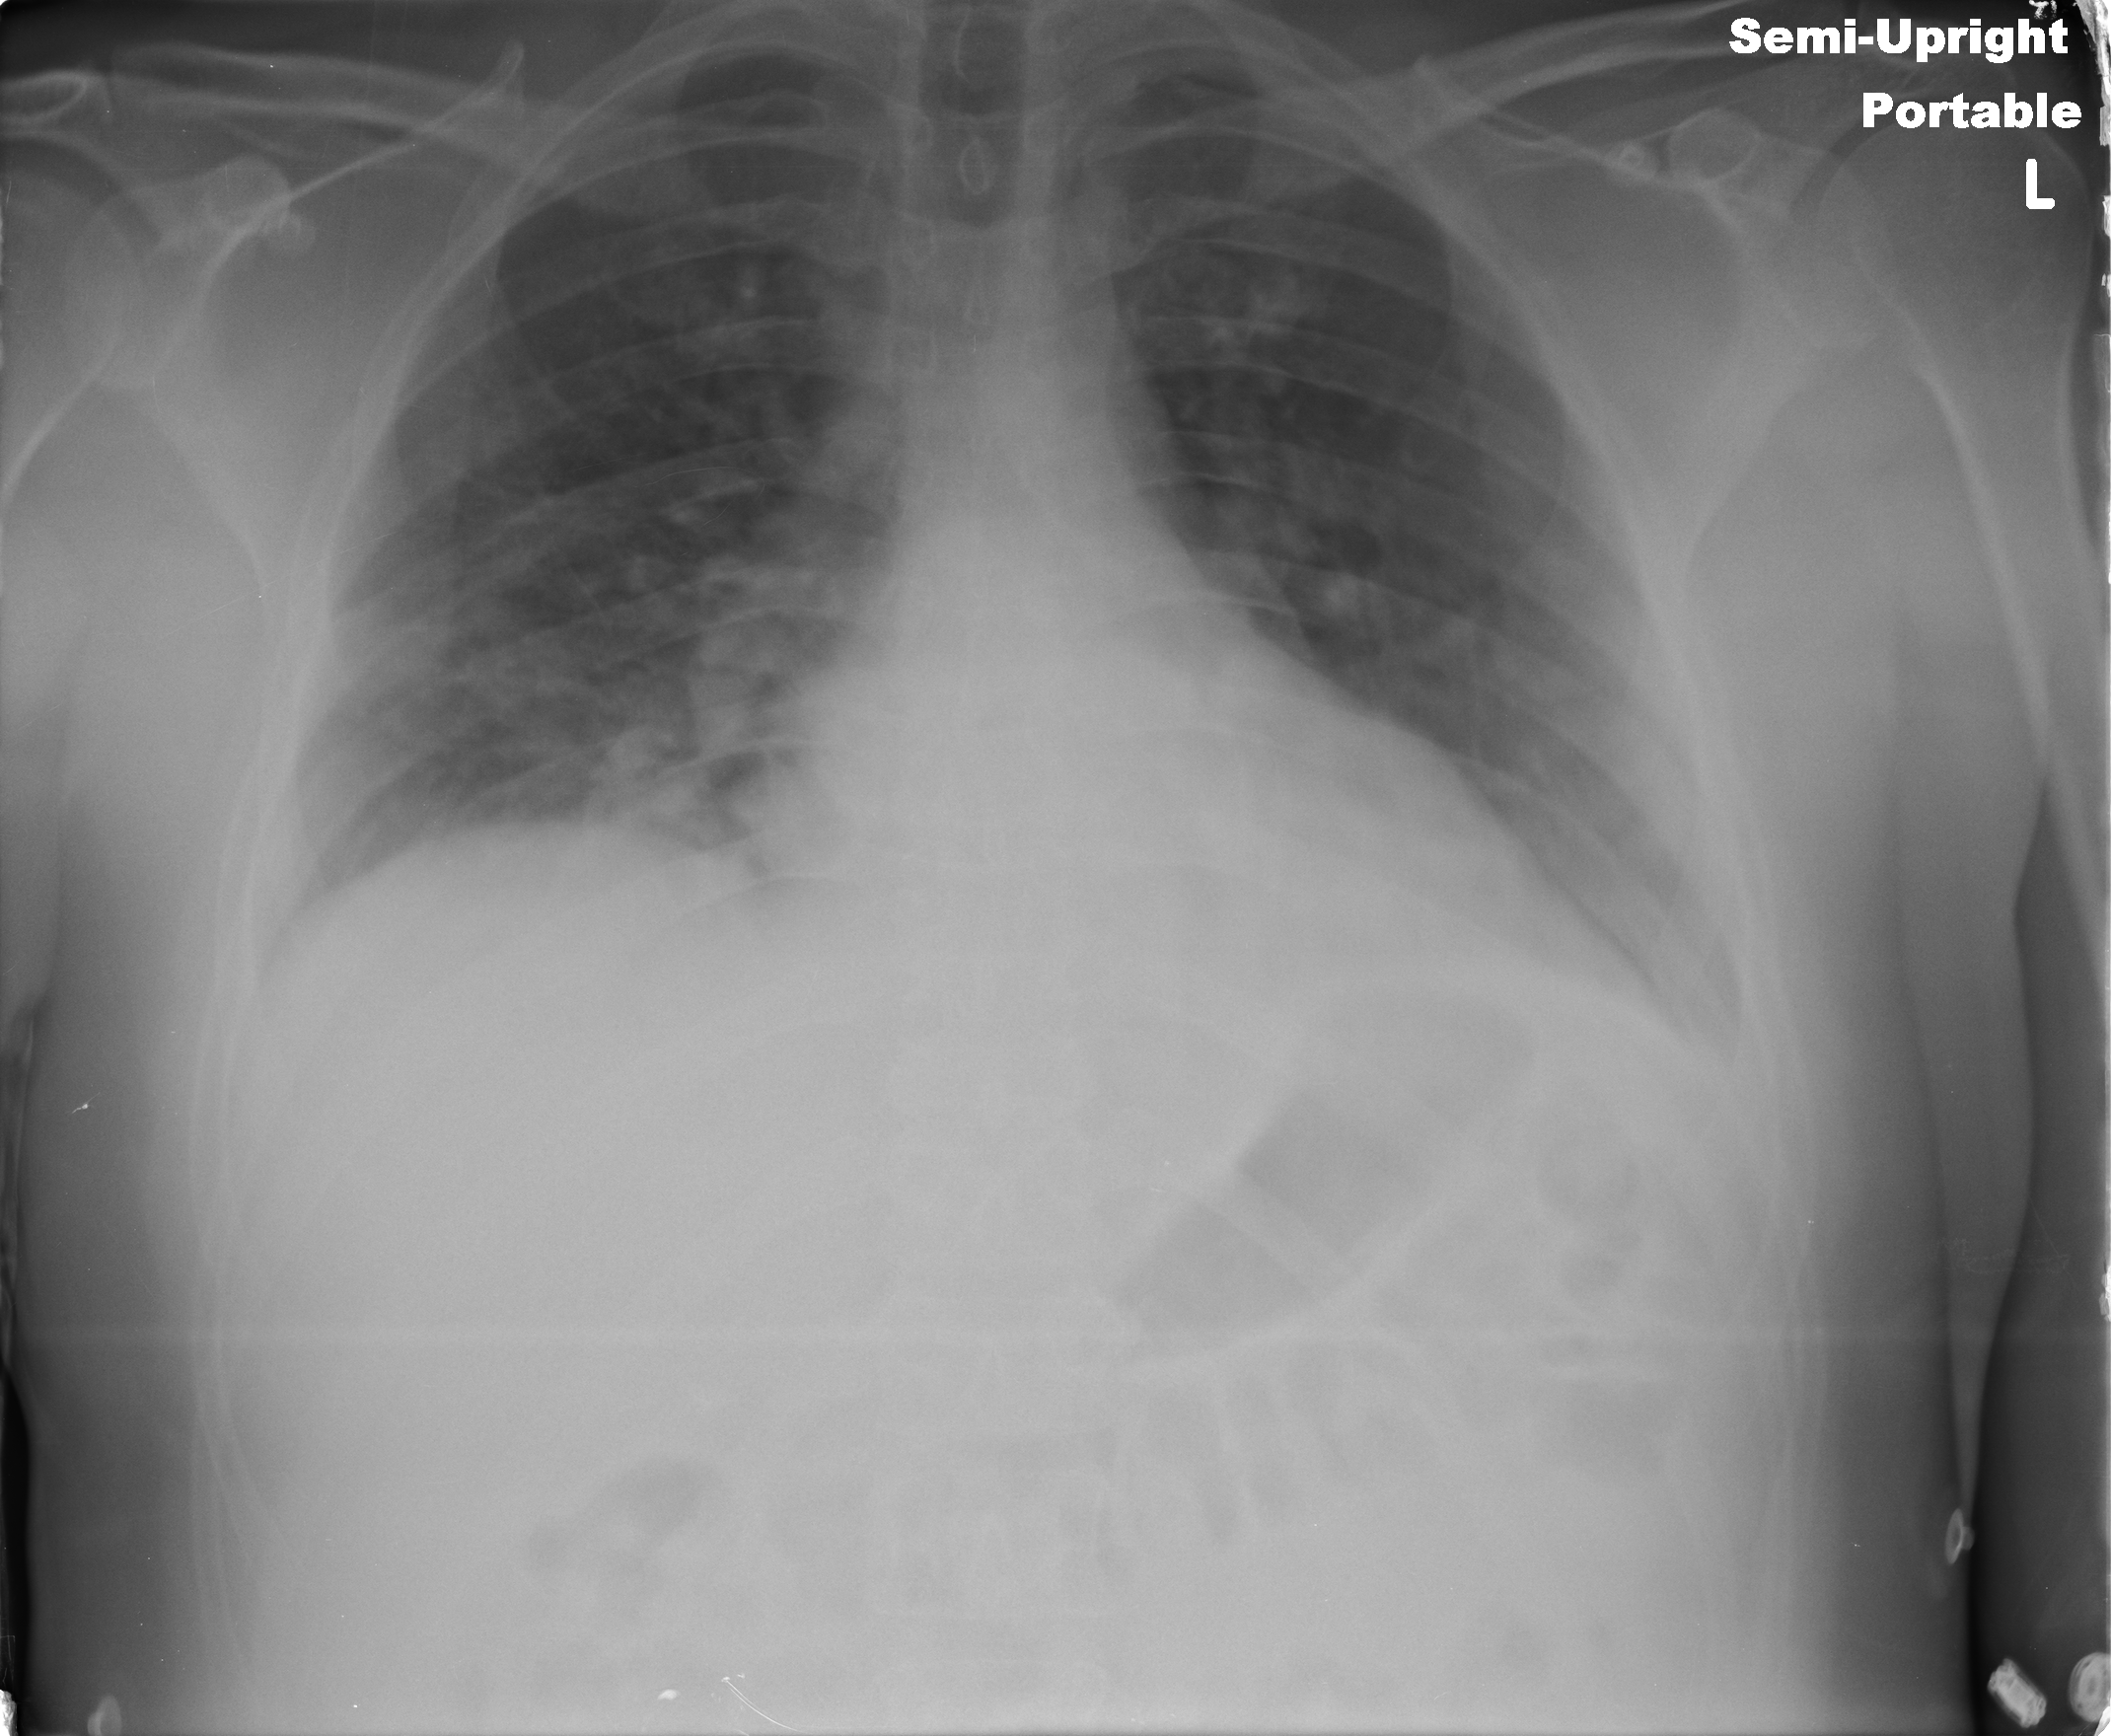
Portable chest radiograph, AP projection. Male patient, age 37 years; imaged 0 days after the COVID-19 diagnosis.
Radiologist's key findings for this exam: mild bibasilar airspace opacities.